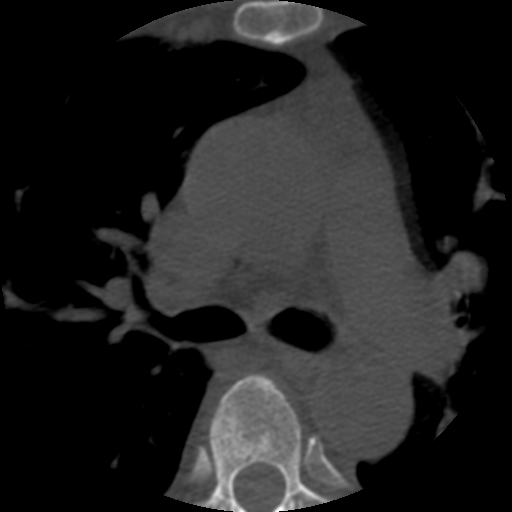
CT including the spine, one axial slice; position 379 of 508 along the scan axis; reconstruction kernel STANDARD; 120 kVp; bone window (W 1800 / L 400 HU); 1.25 mm slice thickness; 512 × 512 image matrix. Patient age 57 years. From the clinical record (not read from this slice): primary cancer: prostate.
Structures marked on this image (semi-automatically segmented with operator editing):
- T5 vertebra: bounding box <205,375,326,512> (left, top, right, bottom; pixels)